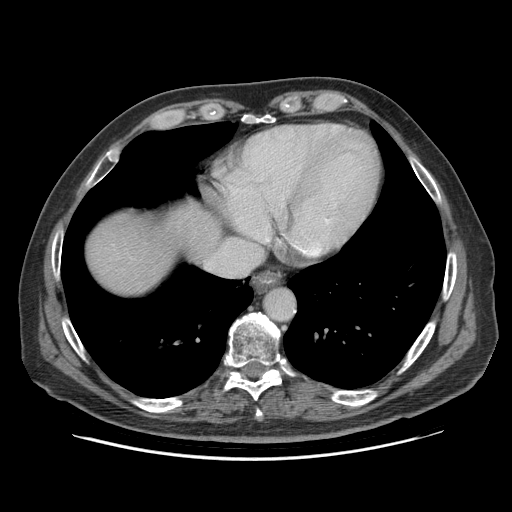
Contrast-enhanced abdominal CT (liver protocol), one axial slice. Reconstruction kernel STANDARD. Soft-tissue window (W 400 / L 40 HU). 2.5 mm slice thickness. 512 × 512 image matrix, field of view 400 × 400 mm. From the clinical record (not read from this slice): diagnosis: hepatocellular carcinoma (patient treated with transarterial chemoembolisation; whether this scan precedes or follows treatment is not stated here); TNM stage (as recorded): Stage-IVB; Child-Pugh class: A.
Annotated regions visible in this slice (semi-automatically segmented with operator editing):
- liver parenchyma outside the tumour (the mass and vessels are separate outlines, so this box may not span the whole liver): bounding box <88,206,220,294> (left, top, right, bottom; pixels)